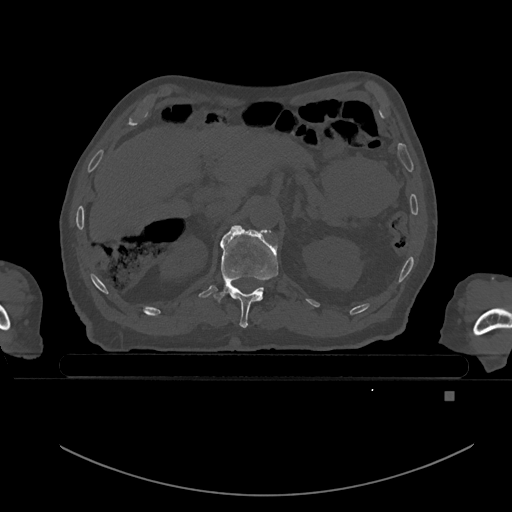
CT including the spine, one axial slice. Slice 15 of 969 in the series (ordered by position). Bone window (W 1800 / L 400 HU). 0.5 mm slice thickness. 512 × 512 image matrix, field of view 456 × 456 mm. Patient: male, 82 years. Case-level facts recorded for this patient, not image findings: primary cancer: prostate; vertebrae with lytic lesions (as recorded): T11, T9, T8, T2.
Structures marked on this image (semi-automatic segmentation, software-assisted and operator-edited):
- T11 vertebra: bounding box (x1, y1, x2, y2) in pixels: (214, 227, 278, 328)